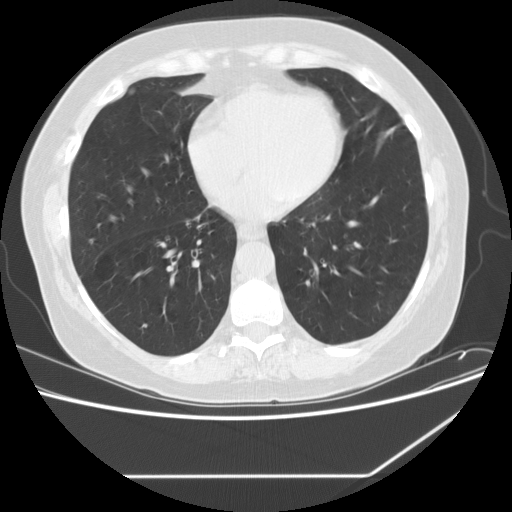
Axial slice from a low-dose chest CT screening exam, second screening round (one year after baseline), lung window (W 1500 / L -600 HU), standard (soft-tissue) reconstruction kernel (STANDARD), 512 × 512 image matrix. Female, age 59 years at enrolment. Current smoker at enrolment.
Expert-annotated lung lesion, bounding box (x1, y1, x2, y2) in pixels: (126, 306, 165, 343). No non-calcified nodule or mass ≥4 mm was recorded by the screening reader at this exam. Official screen result: negative screen, significant abnormalities not suspicious for lung cancer. Later outcome: lung cancer diagnosed 380 days after this screen (after the third annual screen) — non-small cell carcinoma, right lower lobe, poorly differentiated (G3), stage IA (AJCC 6th edition), 15 mm at pathology.